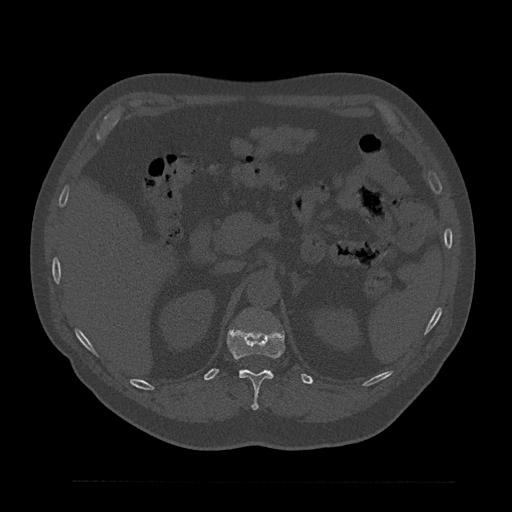
CT including the spine, one axial slice. Position 218 of 797 along the scan axis. 120 kVp. Bone window (W 1800 / L 400 HU). 0.5 mm slice thickness. 512 × 512 image matrix. Patient: male, 61 years. Case-level facts recorded for this patient, not image findings: primary cancer: prostate.
Annotated regions visible in this slice (semi-automatically segmented with operator editing):
- T12 vertebra: bounding box (x1, y1, x2, y2) in pixels: (227, 327, 285, 410)